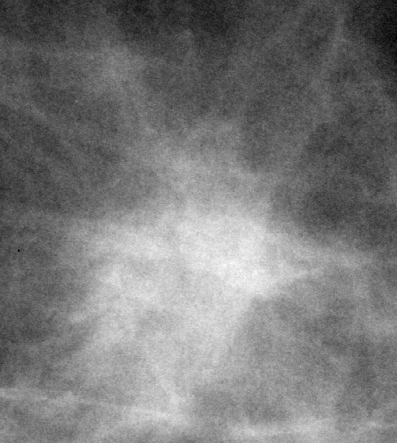
Region of interest cut from a scanned film mammogram (one marked finding); left breast; MLO view; BI-RADS breast density category 2 (scale 1–4).
- Mass, shape architectural distortion, margins spiculated; BI-RADS assessment category 5; pathology (as recorded): malignant.